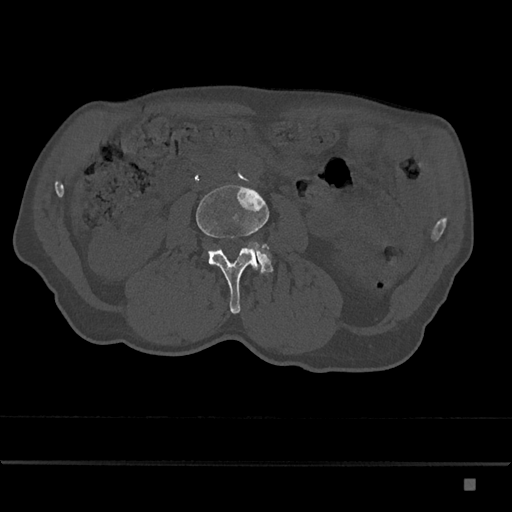
CT including the spine, one axial slice. Slice 394 of 797 in the series (ordered by position). Reconstruction kernel Br40s/3. 120 kVp. Bone window (W 1800 / L 400 HU). 512 × 512 image matrix, field of view 390 × 390 mm. Male patient, age 72 years. From the clinical record (not read from this slice): primary cancer: prostate.
Structures marked on this image (semi-automatically segmented with operator editing):
- L3 vertebra: box from (x=196, y=185) to (x=270, y=314) px
- L4 vertebra: (x=247, y=244)–(x=273, y=275)